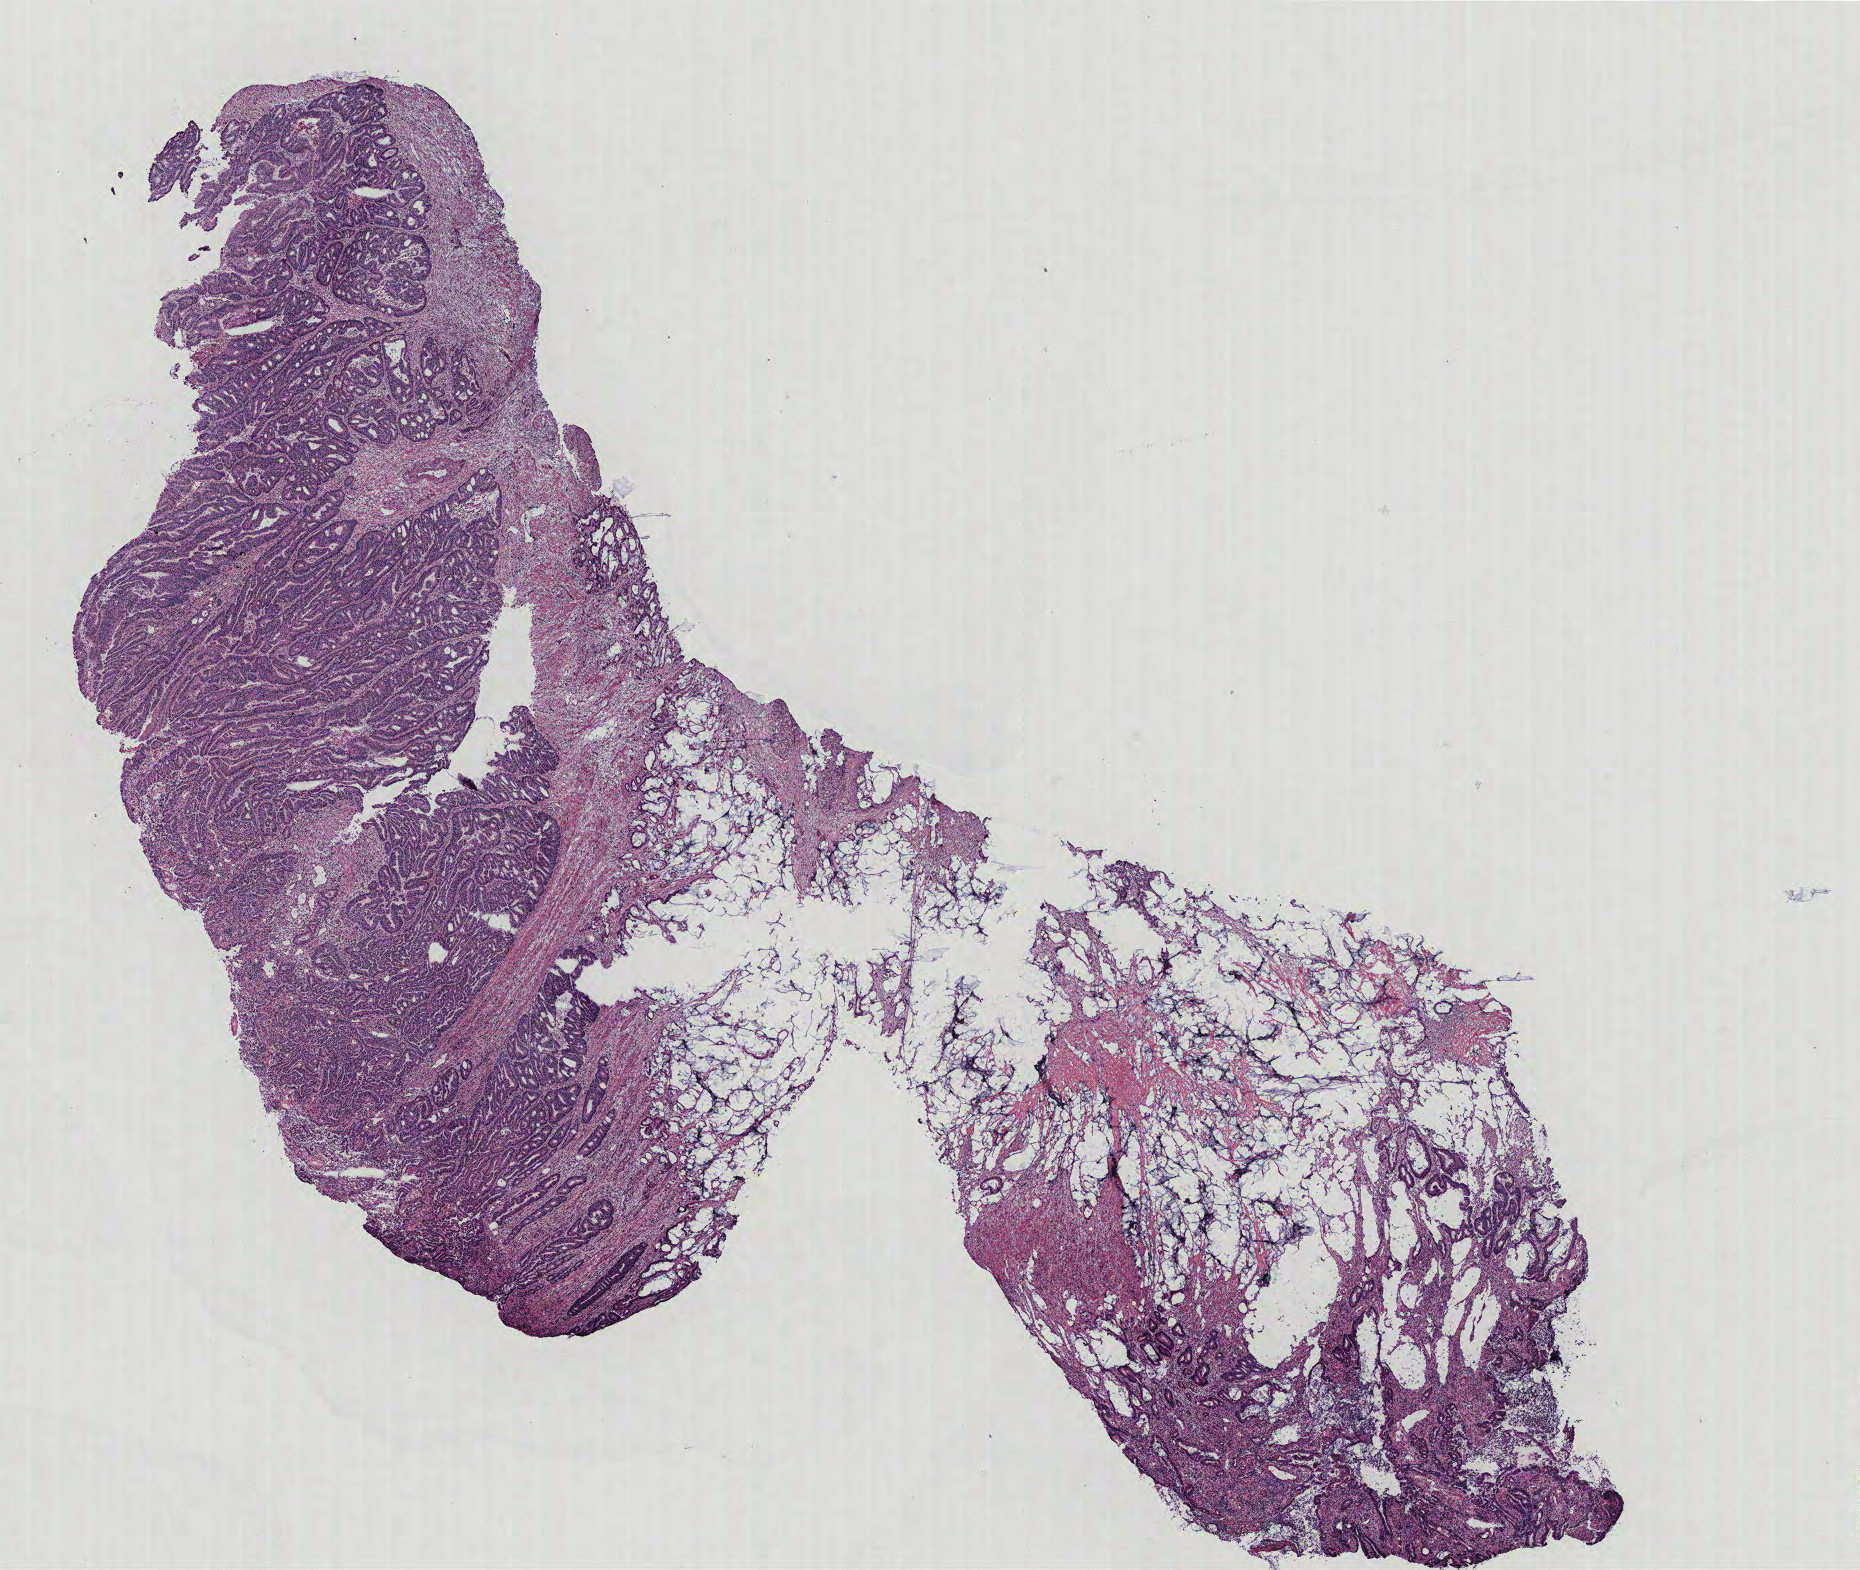
Whole-slide histology image, H&E, a low-resolution overview of the entire scanned area, about 14.9 x 12.6 mm; normal (non-tumour) tissue sample, colon. Patient: female, age 75 years.
This section: normal (non-tumour) tissue from the same patient. Patient diagnosis: Adenocarcinoma, NOS.